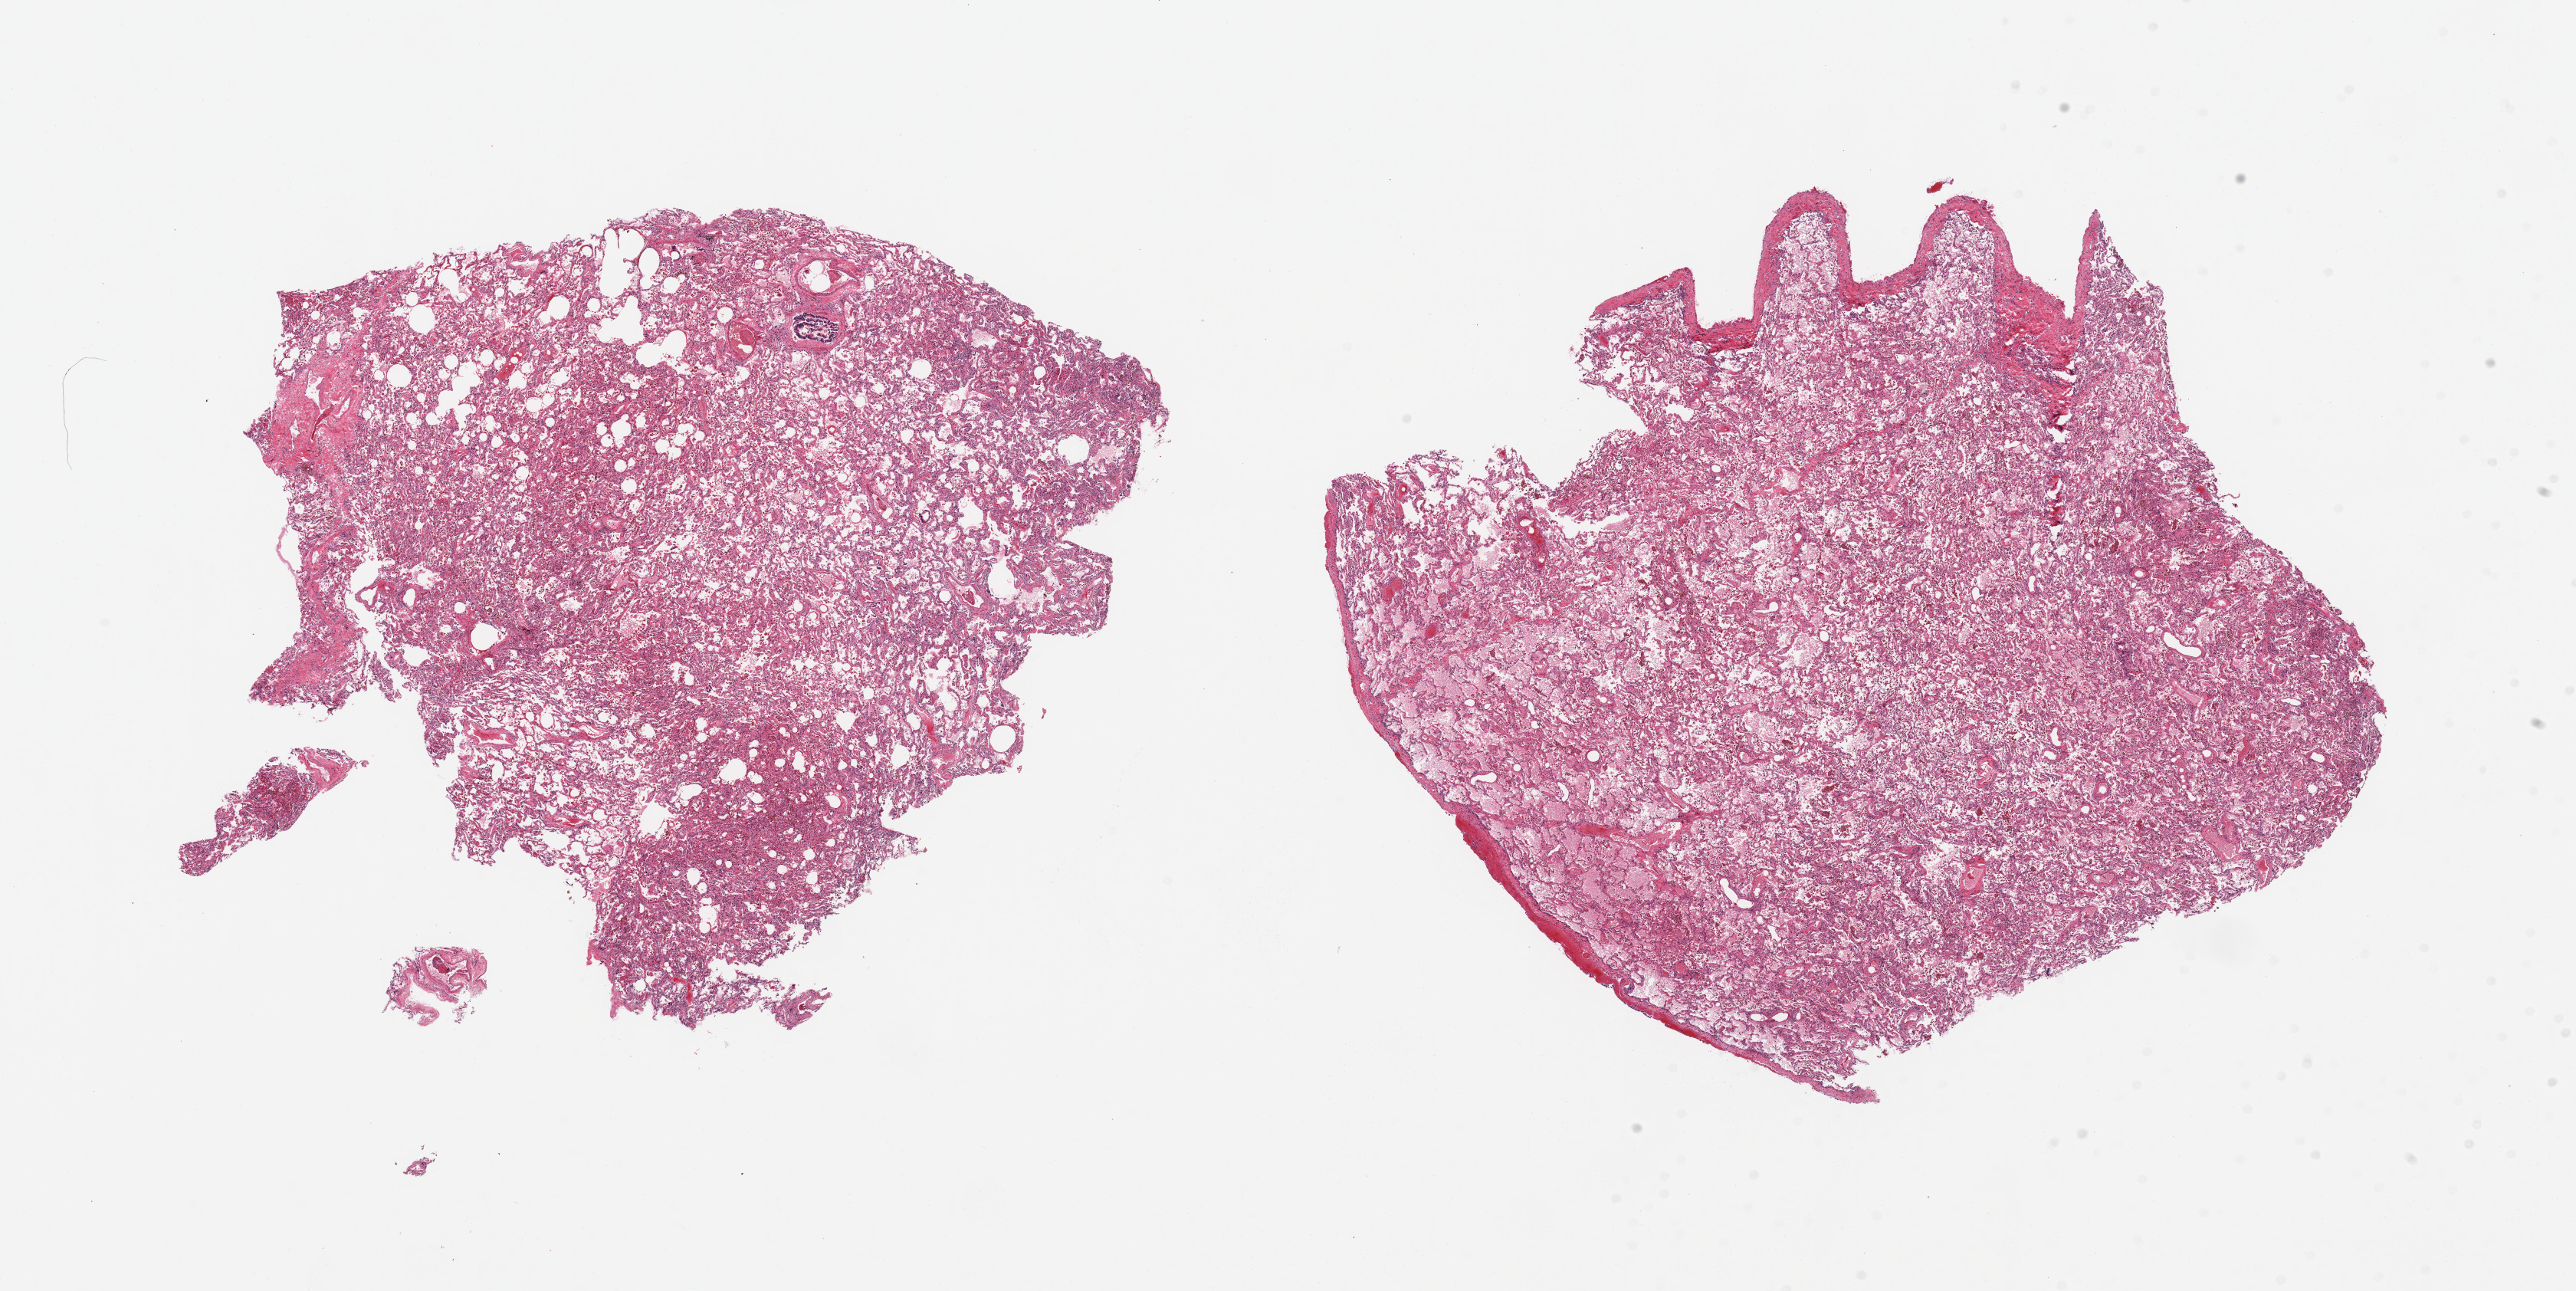
Digitized haematoxylin and eosin-stained section, brightfield — shown as a low-resolution overview of the whole scanned area (about 26.6 x 13.3 mm), PAXgene-fixed paraffin-embedded (PFPE) section, section of lung (target tissue), tissue donor sample. Donor sex: male.
Pathologist's review note for this sample: 2 pieces, moderate edema.